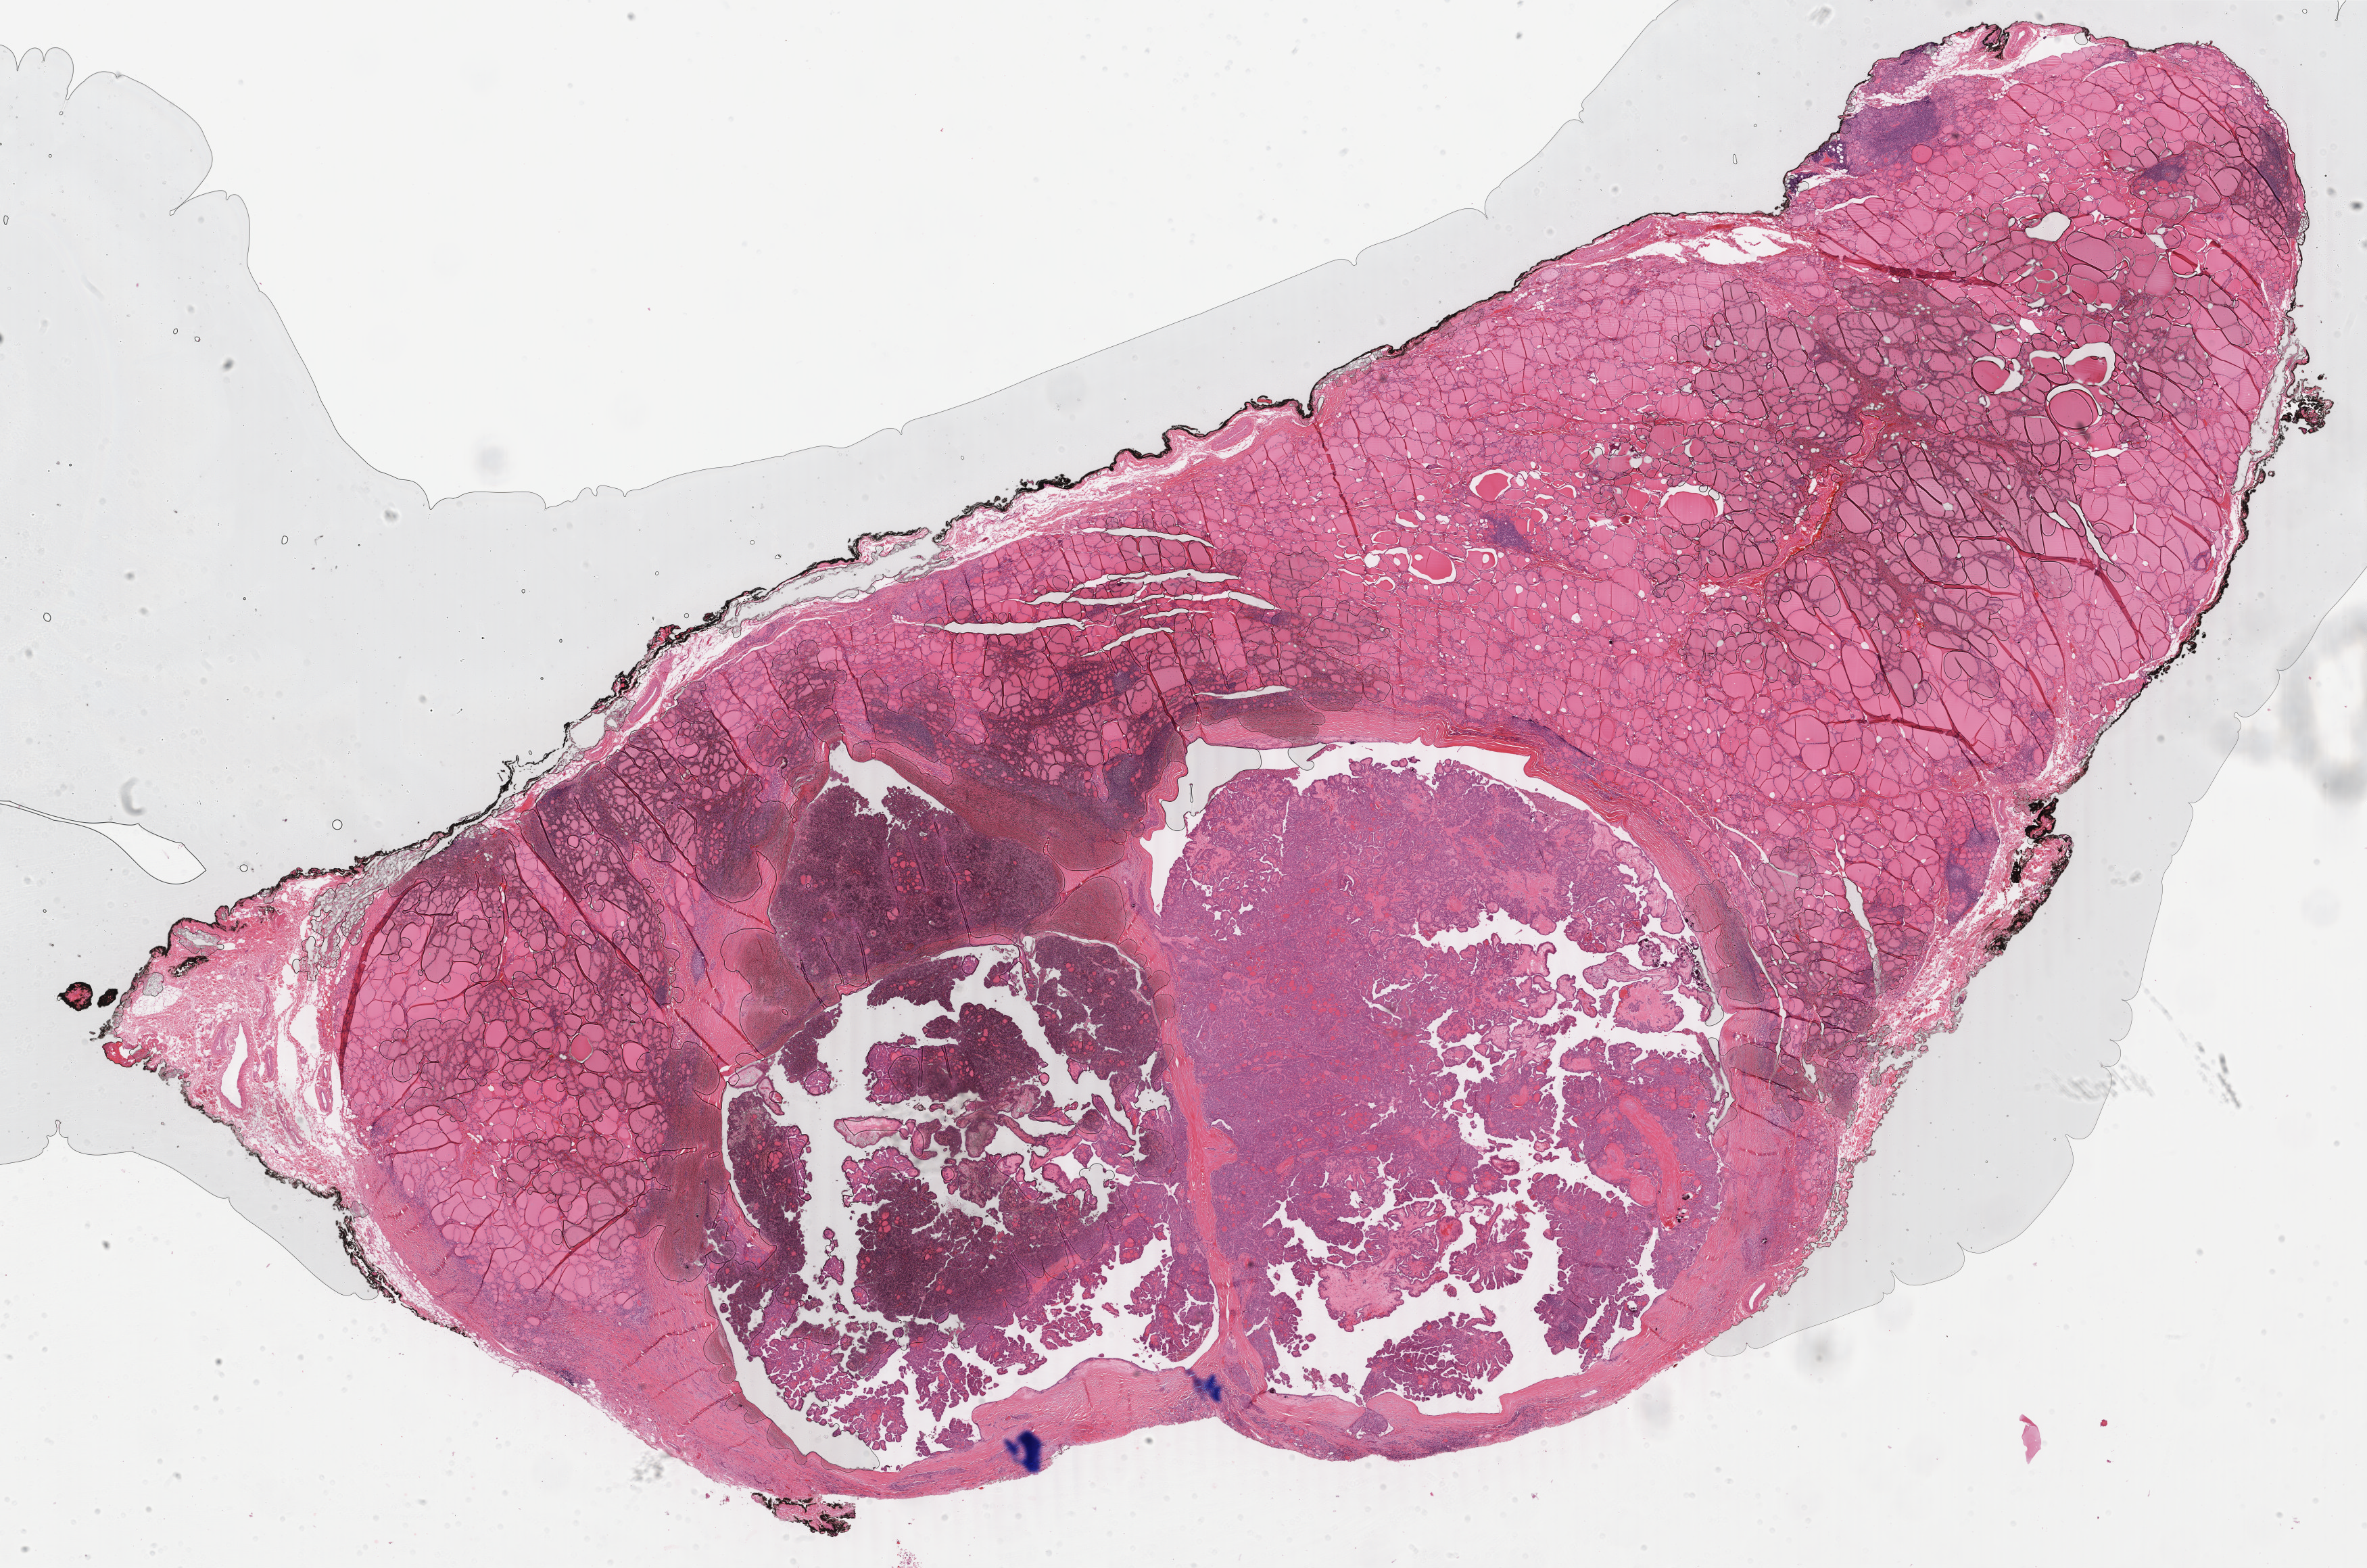
H&E-stained whole-slide image, whole scanned area (about 27.8 x 18.4 mm, acquisition: 40x scan) shown as a low-resolution overview. Formalin-fixed paraffin-embedded (FFPE) diagnostic section. Thyroid, primary tumour sample. Female, age 38 years at initial diagnosis.
TNM: T1 N0 M0. Diagnosis: Papillary adenocarcinoma, NOS (thyroid gland). Laterality: right. AJCC pathologic stage: I. Lymph nodes positive (case pathology): 0 of 17 examined.